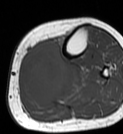
MRI of an extremity soft-tissue mass, one axial slice; position 26 of 68 along the scan axis; MR volume resampled by the dataset authors to the PET/CT grid (not the native acquisition matrix); 123 × 134 image matrix, field of view 120 × 131 mm. Female patient. From the clinical record (not read from this slice): histological type: extraskeletal high grade osteogenic sarcoma; grade: high; site of the primary tumour: left calf.
Annotated regions visible in this slice (expert contour drawn on MRI and transferred to this co-registered scan by the dataset authors):
- gross tumour volume (mass): bounding box <19,41,68,102> (left, top, right, bottom; pixels)